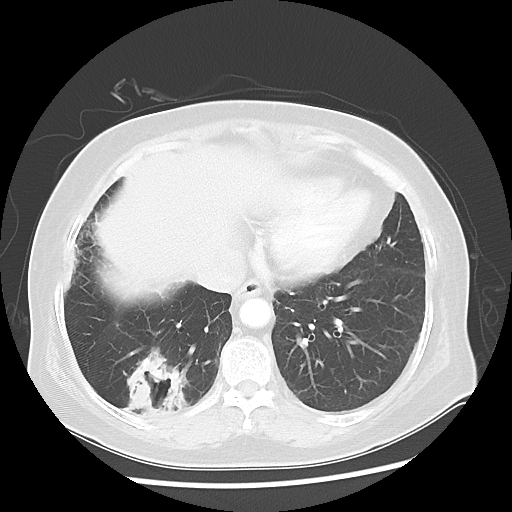
Chest CT, one axial slice; position 17 of 56 along the scan axis; reconstruction kernel LUNG; lung window (W 1500 / L -600 HU); 5 mm slice thickness; 512 × 512 image matrix. Patient: female, 64 years. Case-level facts recorded for this patient, not image findings: clinical TNM (as recorded): Tis N0 M0.
Outlined on this slice (rectangle marked by the reading radiologist):
- lung tumour (recorded histology: adenocarcinoma): bounding box <119,342,197,442> (left, top, right, bottom; pixels)